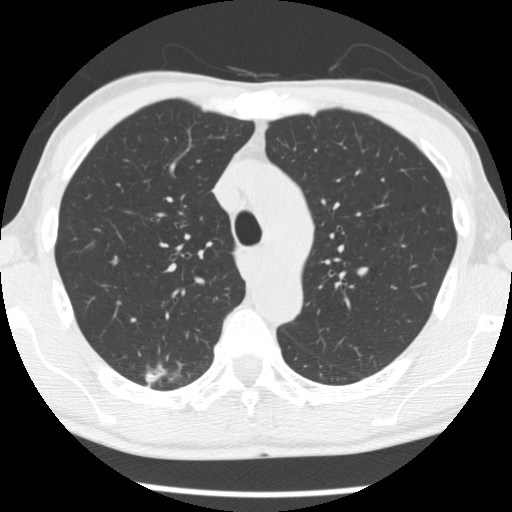
Chest CT (low-dose screening protocol), one axial image. Baseline screening round. Lung window (W 1500 / L -600 HU). 2.5 mm slice thickness. Slice 78 of 277 in the series. 512 × 512 image matrix, field of view 320 × 320 mm. Male, age 66 years at enrolment. Former smoker at enrolment.
- Expert-annotated lung lesion, bounding box (x1, y1, x2, y2) in pixels: (134, 356, 187, 397).
- The screening reader recorded 4 non-calcified nodules or masses ≥4 mm on this exam; which of them this box marks is not recorded.
- Official screen result: positive, change unspecified: nodule(s) >= 4 mm or enlarging nodule(s), mass(es), or other non-specific abnormalities suspicious for lung cancer.
- Later outcome: lung cancer diagnosed 503 days after this screen — adenocarcinoma, NOS, right upper lobe, undifferentiated (G4), stage IA (AJCC 6th edition), 20 mm at pathology.